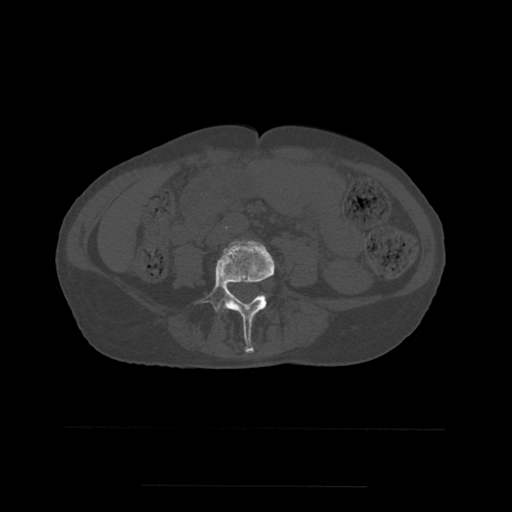
CT including the spine, one axial slice. Slice 166 of 544 in the series (ordered by position). Bone window (W 1800 / L 400 HU). 1.25 mm slice thickness. 512 × 512 image matrix, field of view 350 × 350 mm. Patient age 58 years. Case-level facts recorded for this patient, not image findings: primary cancer: lung.
Annotated regions visible in this slice (semi-automatically segmented with operator editing):
- L4 vertebra: bounding box [x1, y1, x2, y2] px = [197, 241, 275, 354]